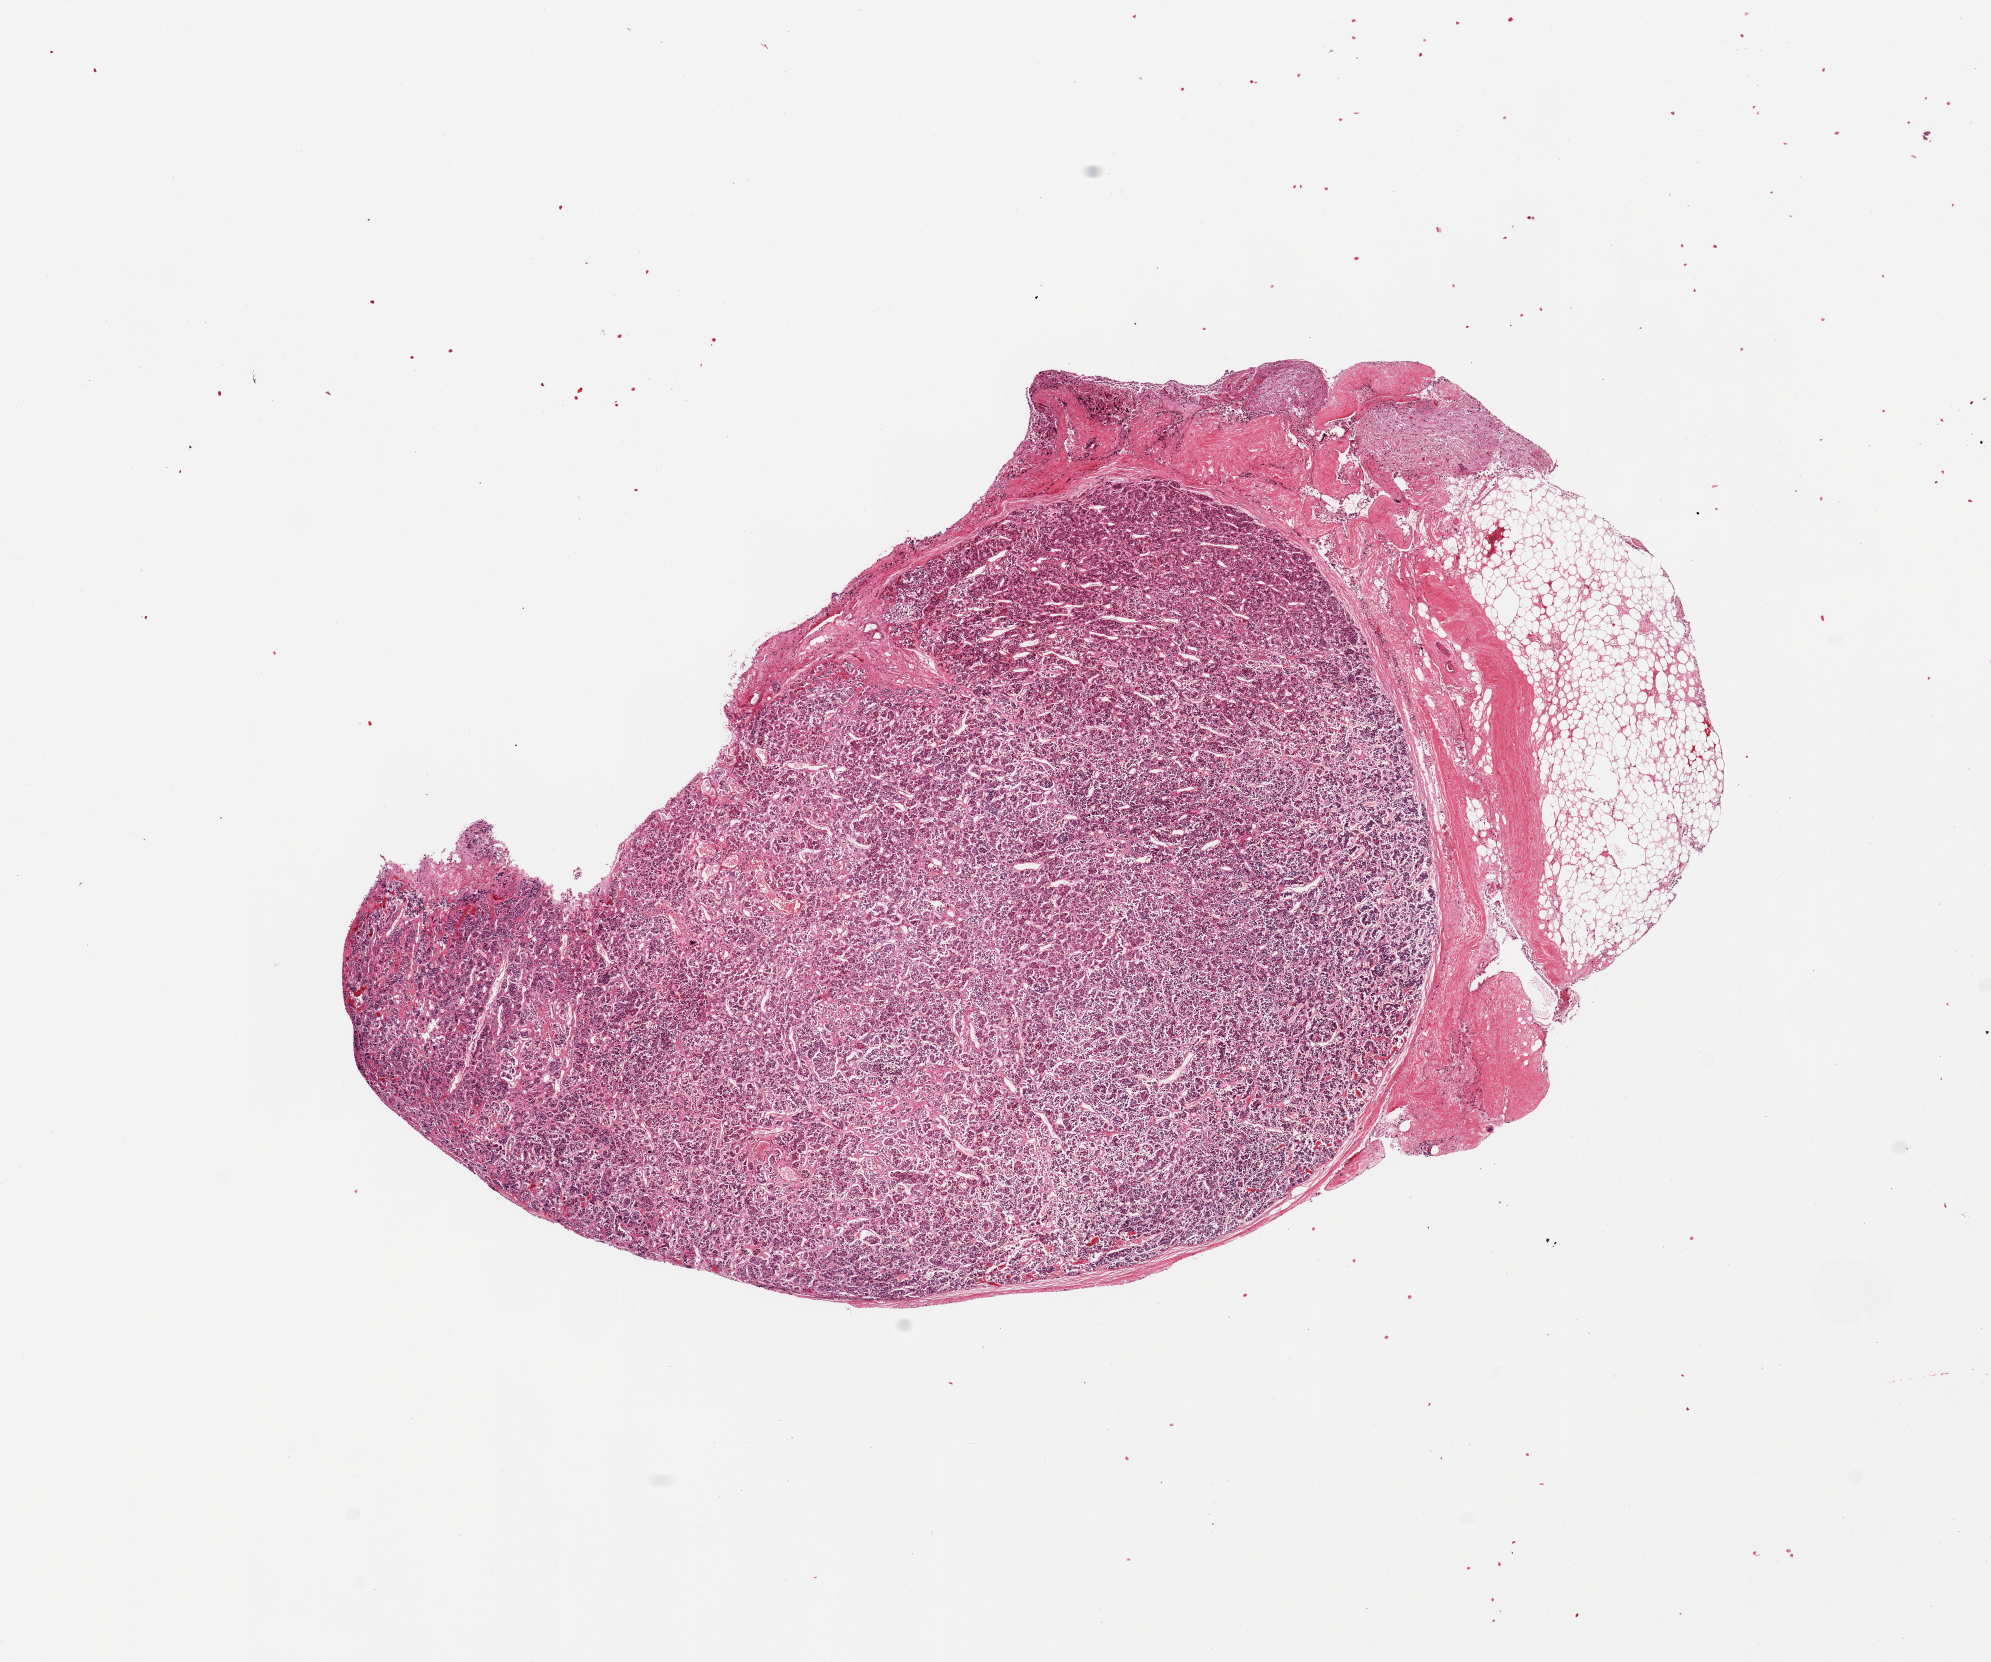
Digitized haematoxylin and eosin-stained section — whole scanned area (about 15.8 x 13.1 mm, slide scanned at 20x) shown as a low-resolution overview; PAXgene-fixed paraffin-embedded (PFPE) section; sampled site (target tissue): pituitary; donor tissue sample.
Pathologist's review note for this sample: 1 piece; mostly adenohypophysis; small amount of posterior lobe and 4x1mm external fat.